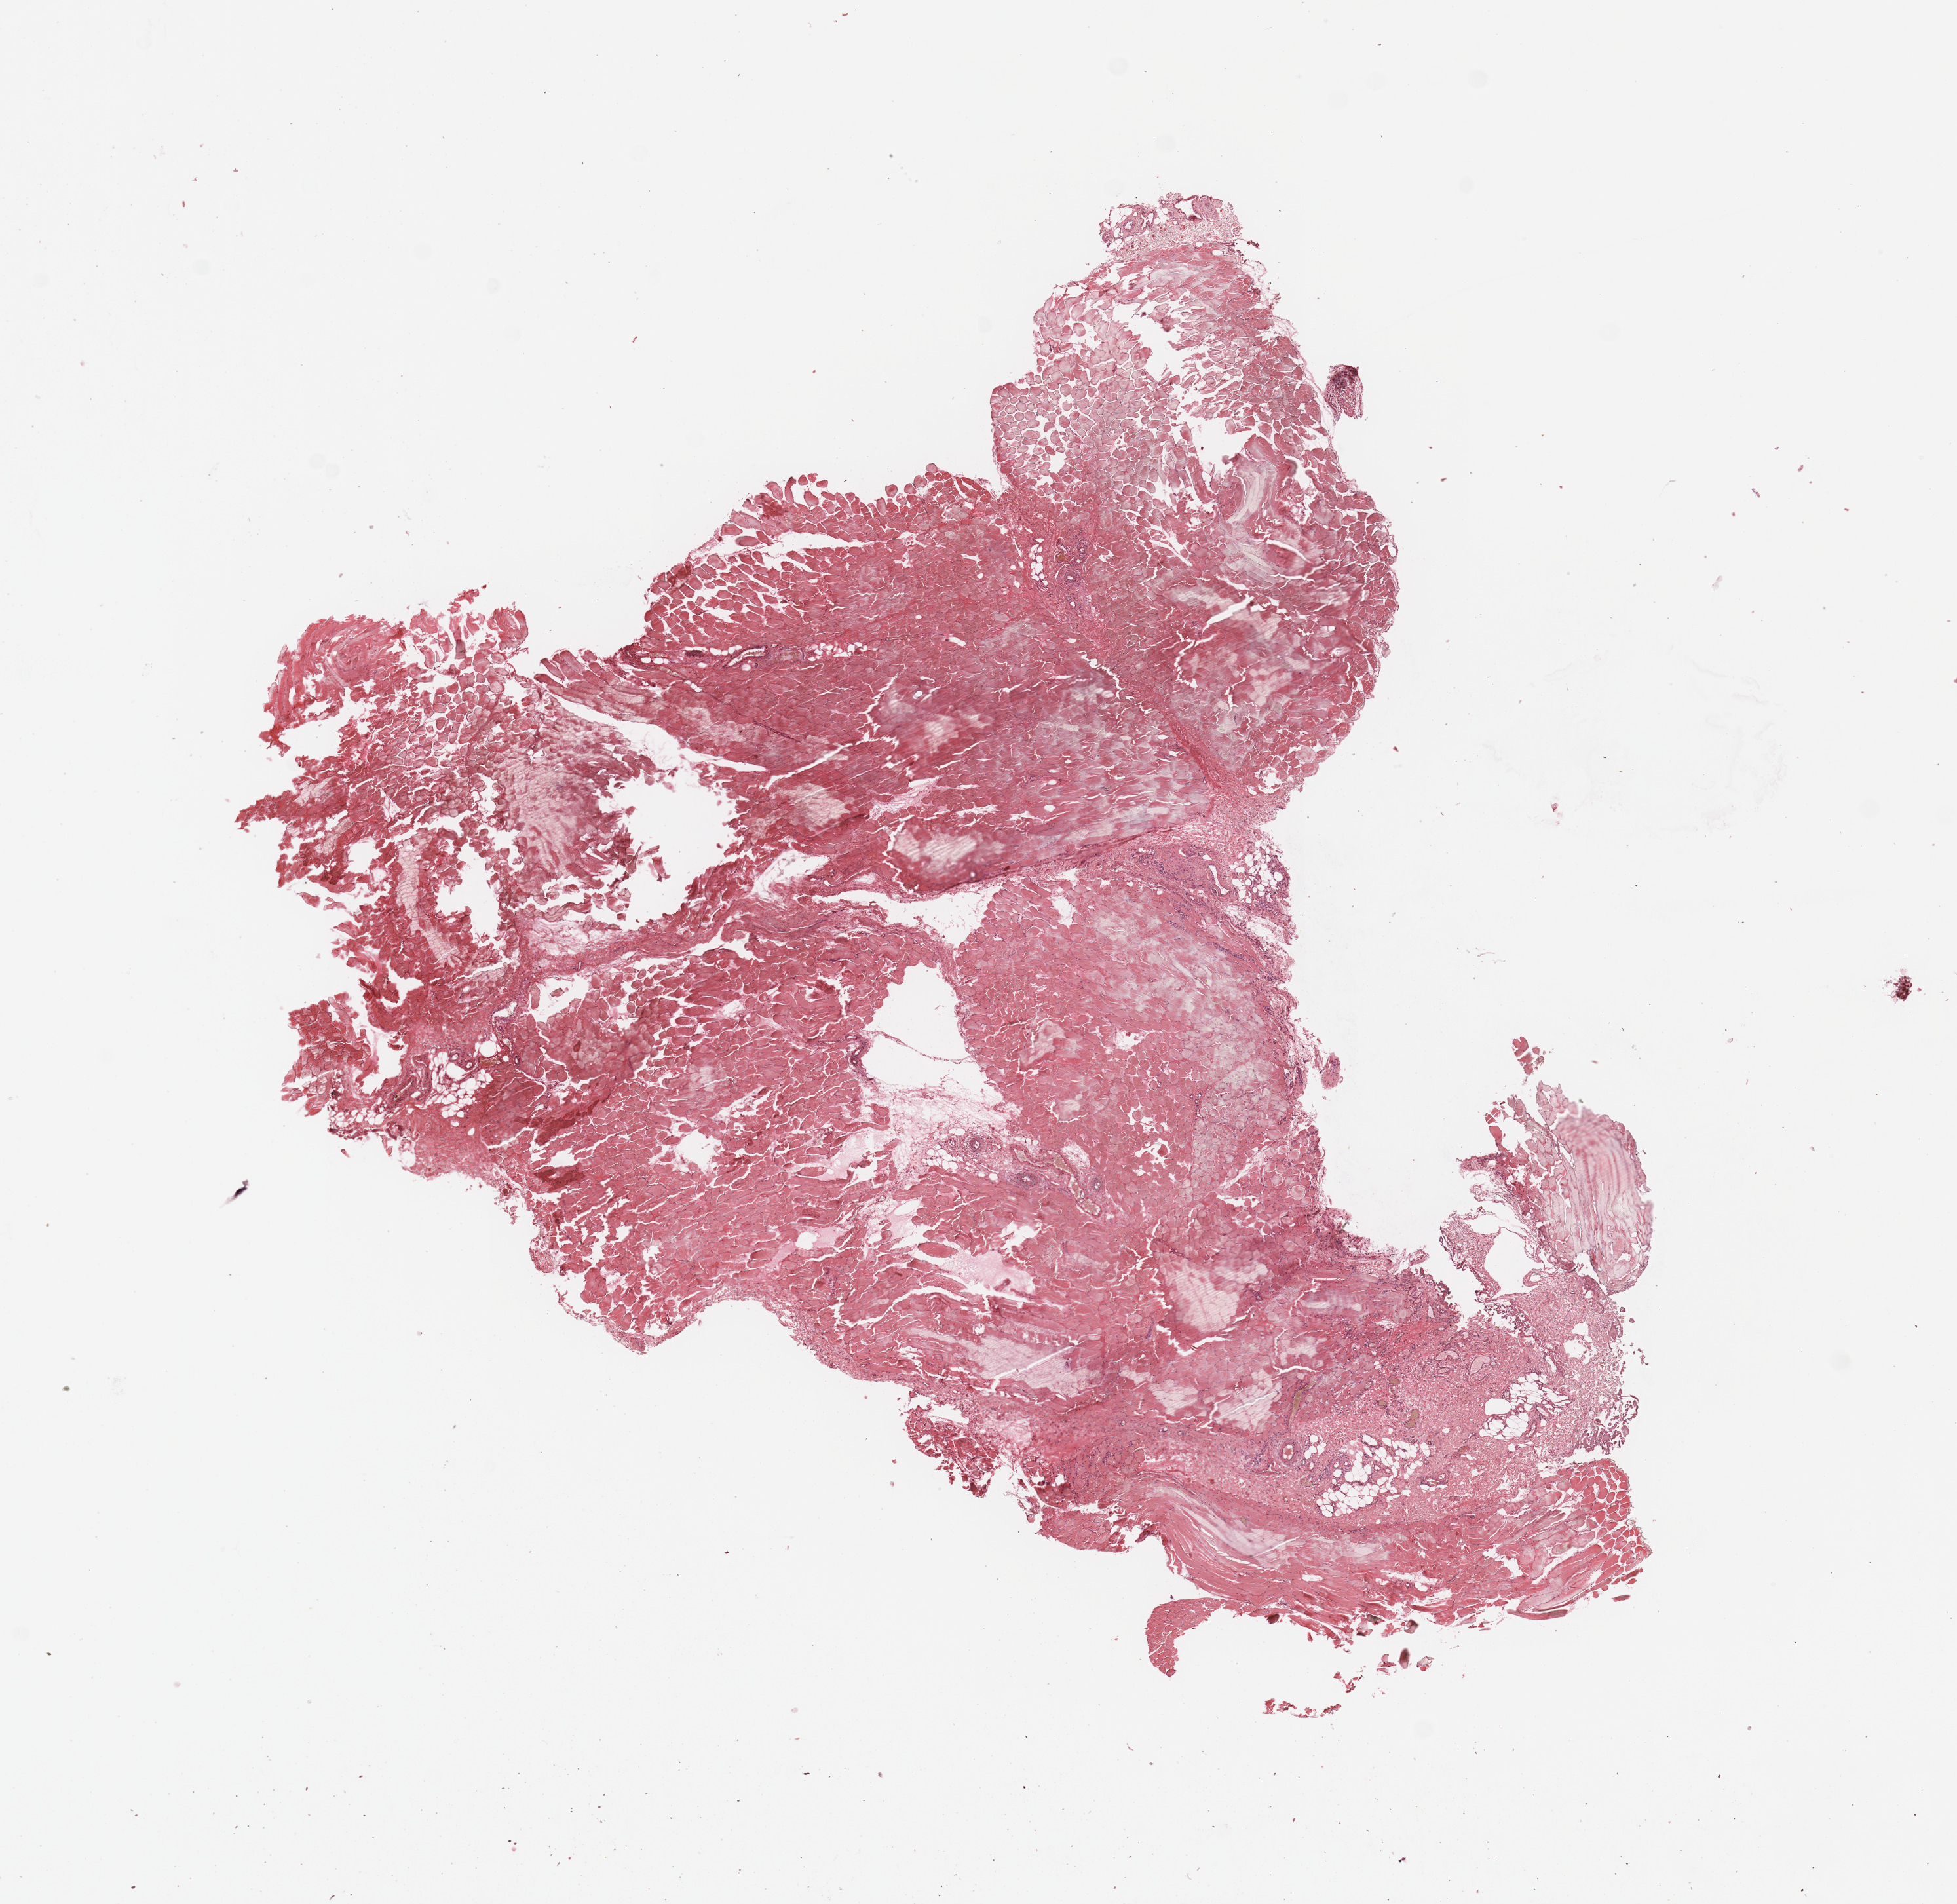
Hematoxylin and eosin (H&E) stained whole-slide image — a low-resolution overview of the entire scanned area, about 11.8 x 11.5 mm; normal (non-tumour) tissue sample. 53-year-old male patient.
This section: normal (non-tumour) tissue from the same patient. Patient diagnosis (cohort enrolment): sarcoma (site not recorded at cohort level).